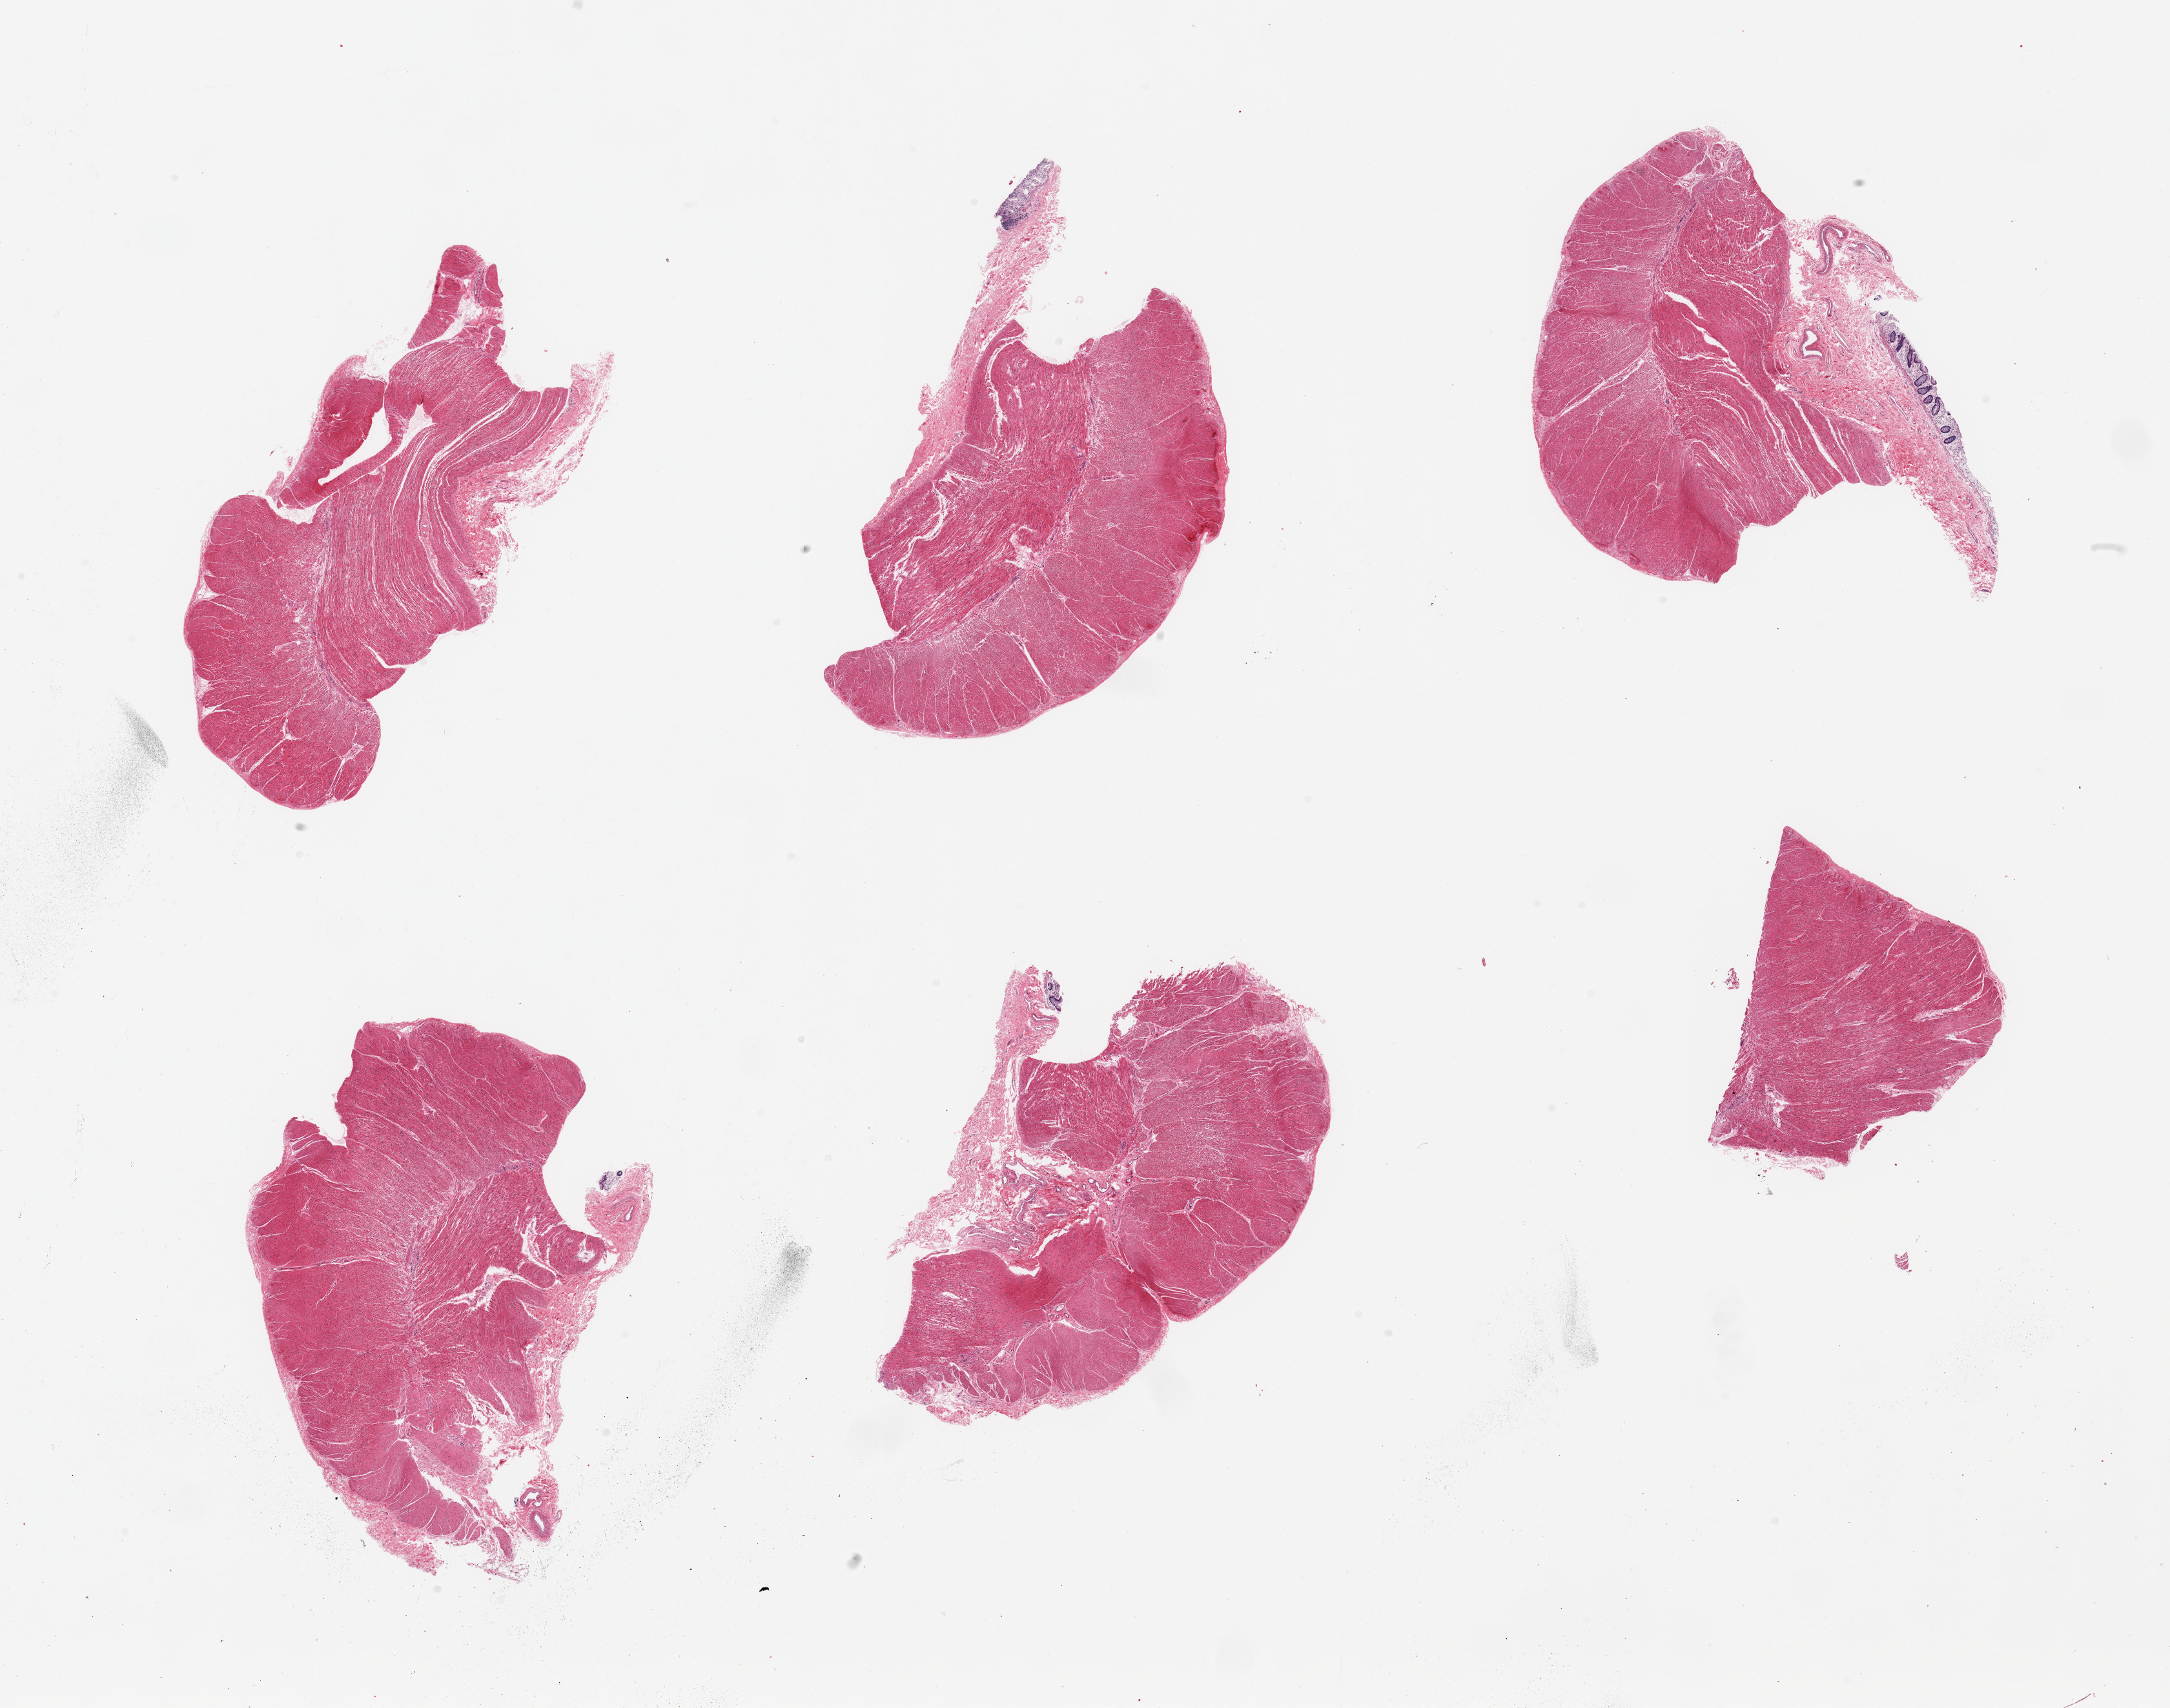
Digitized hematoxylin and eosin (H&E)-stained section, low-resolution overview of the scanned area, about 26.6 x 20.9 mm (slide scanned at 20x); PAXgene-fixed paraffin-embedded (PFPE) section; sampled site (target tissue): sigmoid colon; tissue donor sample. Female donor.
Pathologist's review note for this sample: 6 pieces; target muscularis, small strip of residual mucosa.